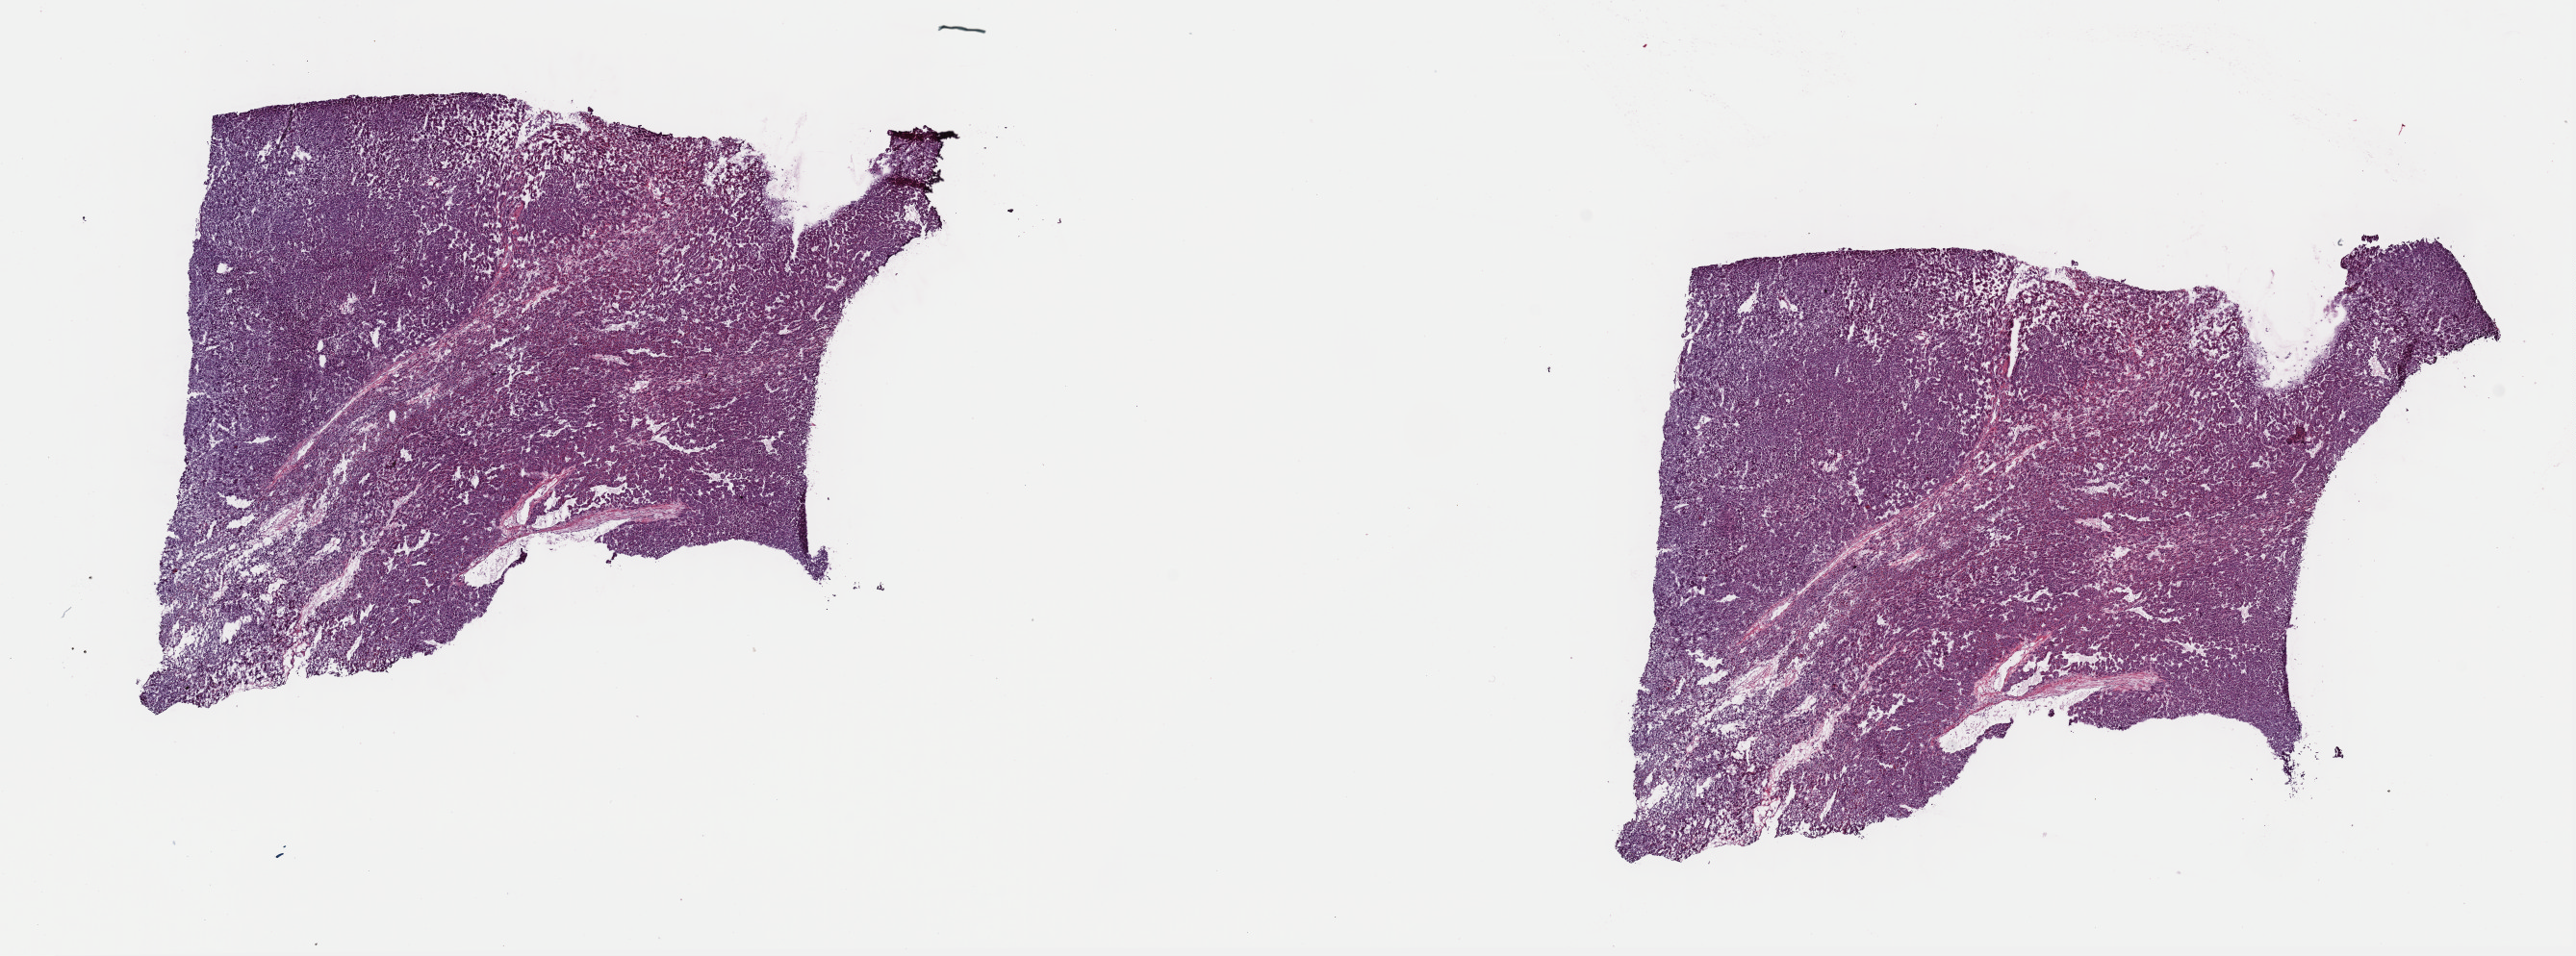
Whole-slide histology image, Hematoxylin and eosin (H&E) stained — a low-resolution overview of the entire scanned area, about 21.1 x 7.9 mm (from a 40x scan); frozen section from the top of the tissue portion; primary tumour sample from the liver. Male patient; age at initial diagnosis 72 years. Histologic grade: G2 (moderately differentiated). Pathologist review of this section (percent, as recorded): tumour cells 90%, tumour nuclei 100%, normal cells 0%, stromal cells 10%, necrosis 0%. Inflammatory infiltration, as recorded: lymphocyte infiltration 1%, monocyte infiltration 1%, neutrophil infiltration 0%.
Histologic diagnosis: Hepatocellular carcinoma, NOS. AJCC pathologic stage: I (7th edition).